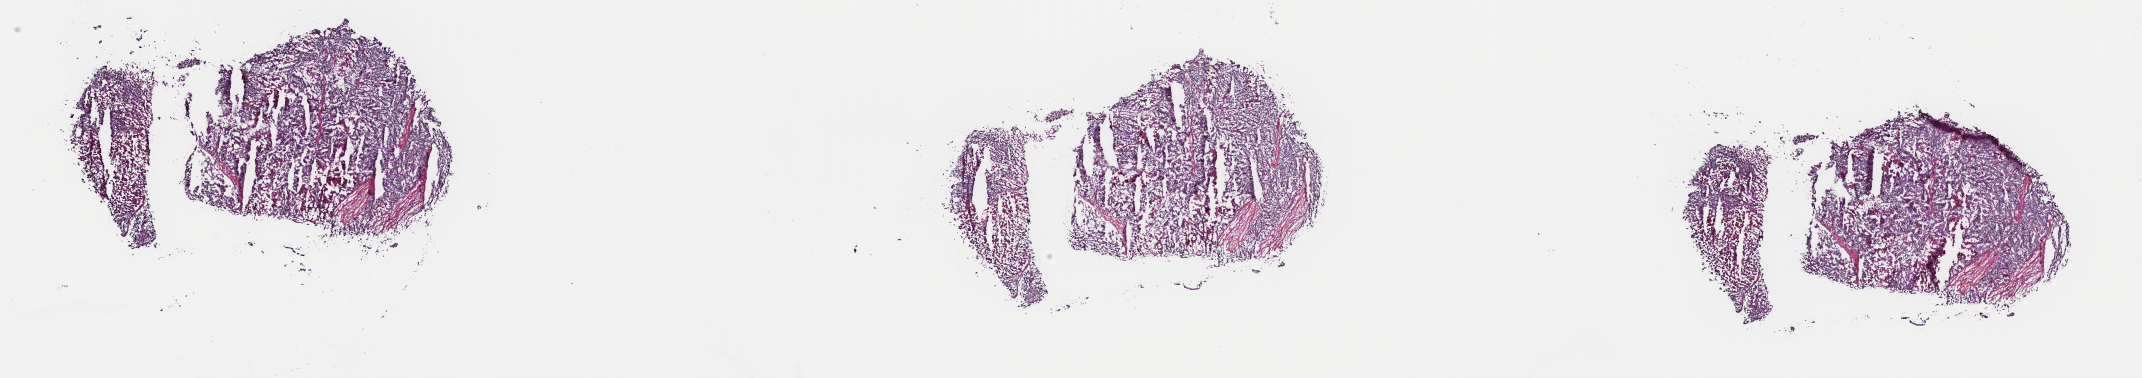
Whole-slide histology image, H&E-stained, low-resolution overview of the scanned area, about 33.8 x 6.0 mm (acquisition: 40x scan). Frozen section from the top of the tissue portion. Adrenal cortex, primary tumour sample. Patient: male, age at initial diagnosis 65 years. Composition of this section per pathologist review: tumour cells 99%, tumour nuclei 99%, normal cells 0%, stromal cells 1%, necrosis 0%. Infiltration values recorded for this section: lymphocyte infiltration 0%, monocyte infiltration 0%, neutrophil infiltration 0%.
Diagnosis: Adrenal cortical carcinoma (cortex of adrenal gland). Lymph nodes positive (case pathology): 6 of 6 examined.